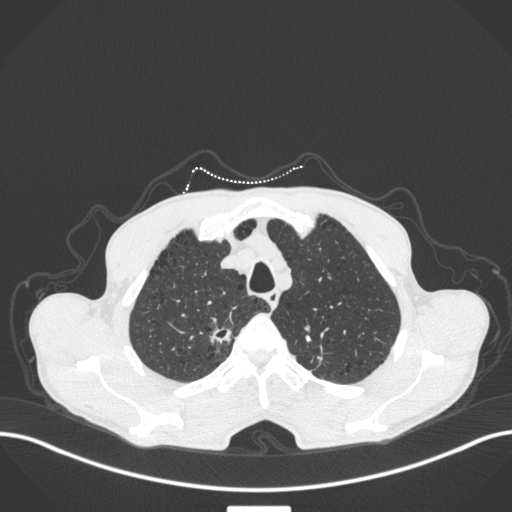
Chest CT, one axial slice. Slice 358 of 445 in the series (ordered by position). 120 kVp. Lung window (W 1500 / L -600 HU). 512 × 512 image matrix, field of view 400 × 400 mm. Male patient, age 70 years. From the clinical record (not read from this slice): clinical TNM (as recorded): T1a N0 M0; histopathological grade: G1-2.
Structures marked on this image (bounding box drawn by a radiologist):
- lung tumour (recorded histology: adenocarcinoma): bounding box <209,321,239,350> (left, top, right, bottom; pixels)